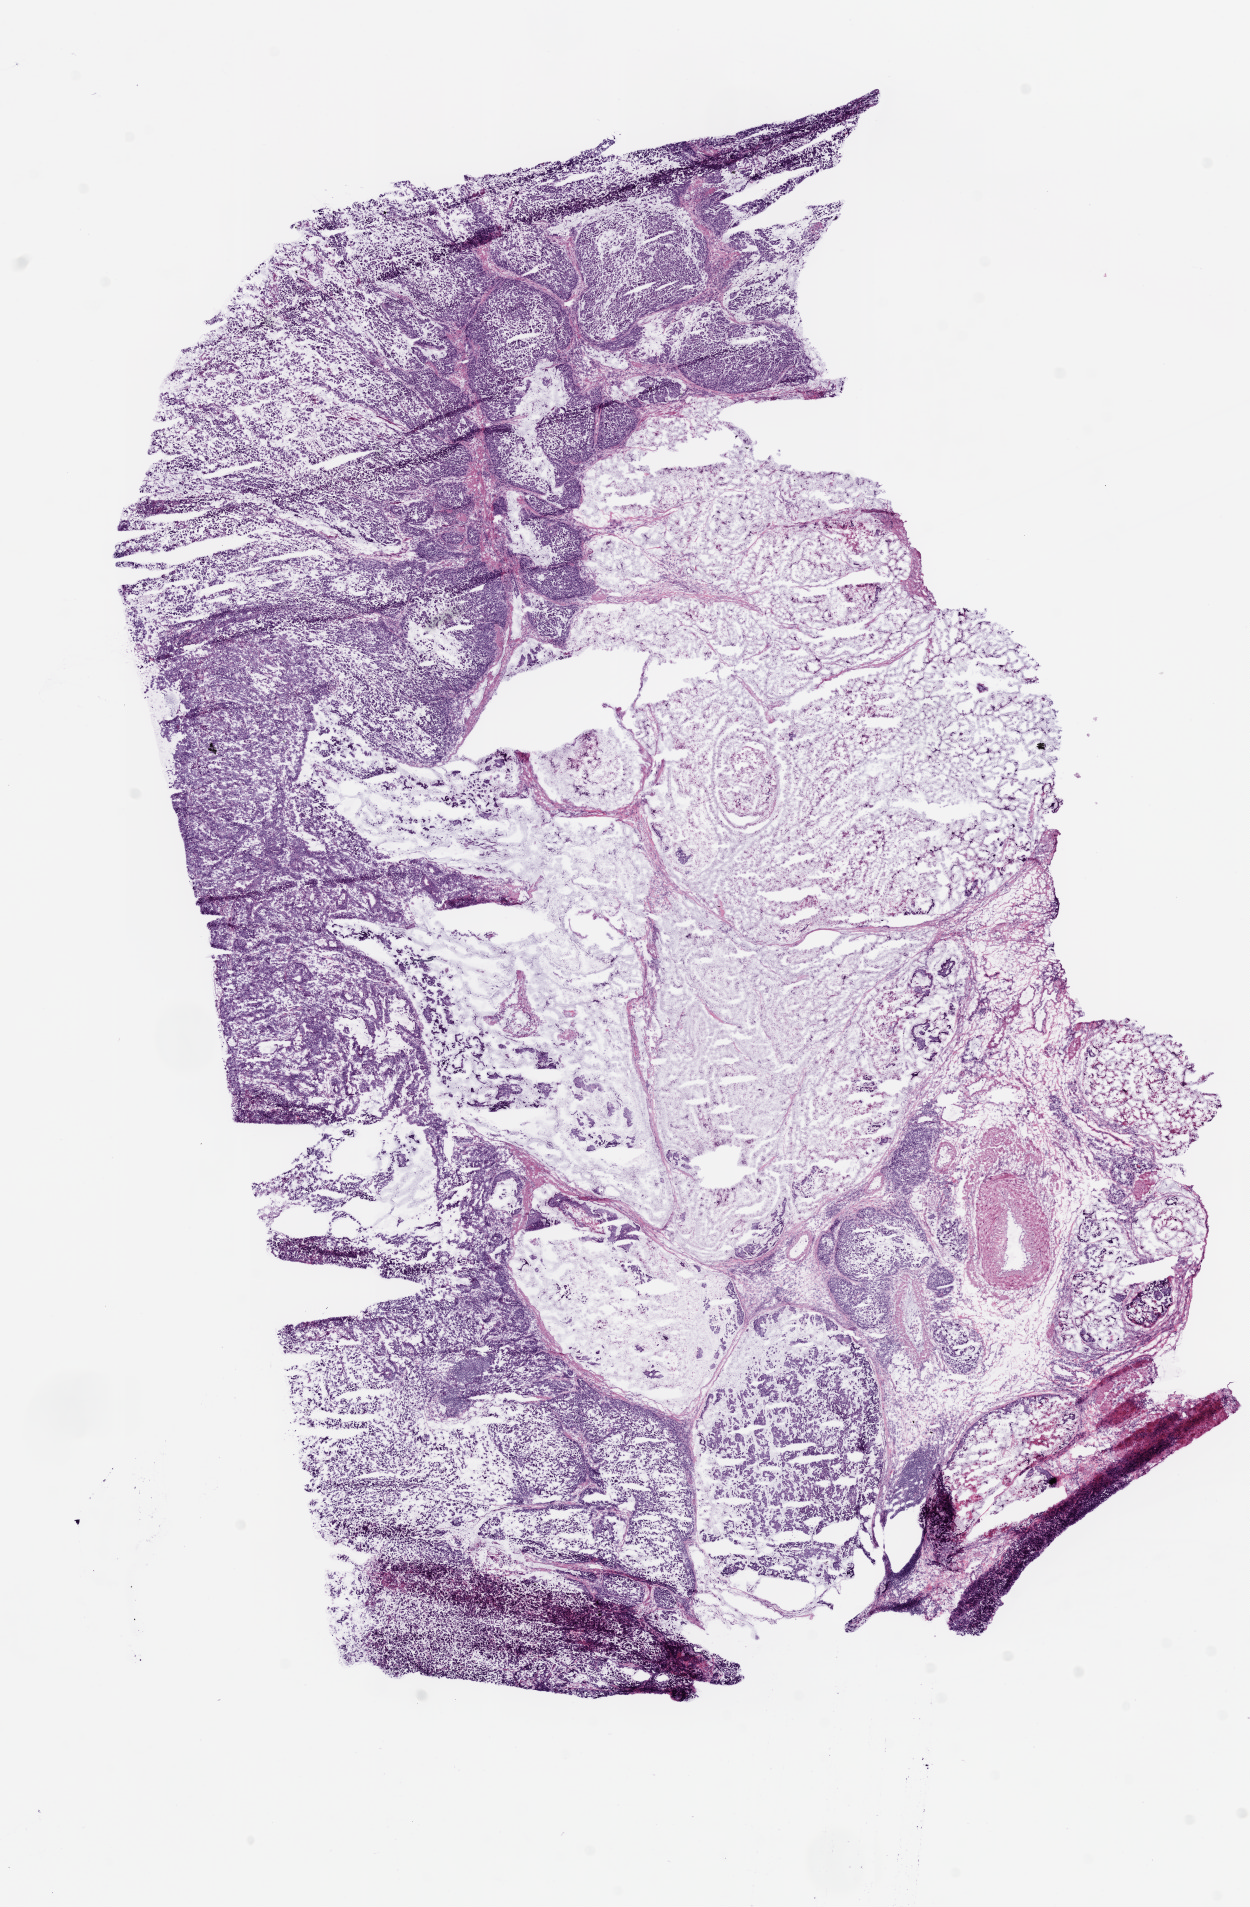
Digitized H&E-stained tissue section (whole slide), whole scanned area (about 10.0 x 15.3 mm, from a 20x scan) shown as a low-resolution overview. Frozen section from the bottom of the tissue portion. Primary tumour sample from the stomach. Male patient; age at initial diagnosis 76 years. Histologic grade: G3 (poorly differentiated). Pathologist review of this section (percent, as recorded): tumour cells 95%, tumour nuclei 80%, normal cells 0%, stromal cells 5%, necrosis 0%.
• AJCC pathologic stage: IIIA
• TNM: T2b N2 M0
• histologic diagnosis: Adenocarcinoma, intestinal type (body of stomach)
• lymph nodes positive (case pathology): 15 of 37 examined